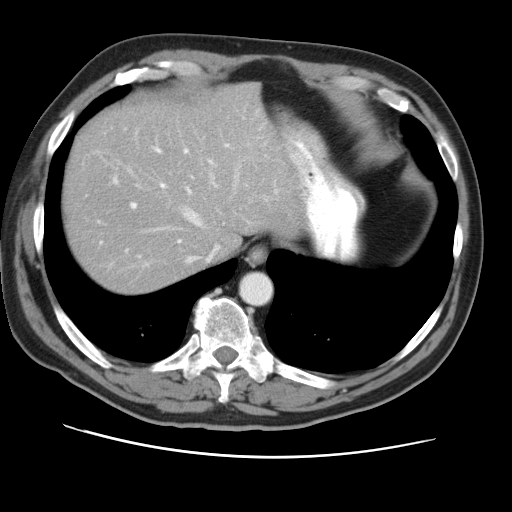
Contrast-enhanced abdominal CT, one axial slice. Position 40 of 49 along the scan axis. 120 kVp. Intravenous contrast given. Soft-tissue window (W 400 / L 40 HU). 5 mm slice thickness. 512 × 512 image matrix, field of view 374 × 374 mm. Male patient, age 59 years. Case-level facts recorded for this patient, not image findings: diagnosis: colorectal cancer liver metastases, imaged before liver resection; multiple liver metastases: yes; largest metastasis: 6.3 cm; disease in both lobes: yes.
Structures marked on this image (expert manual segmentation):
- hepatic veins: bounding box (x1, y1, x2, y2) in pixels: (144, 163, 240, 261)
- liver: (65, 84, 303, 293)
- planned liver remnant (the part of the liver to remain after resection): (65, 84, 303, 293)
- portal vein (with intrahepatic branches): (112, 144, 228, 258)